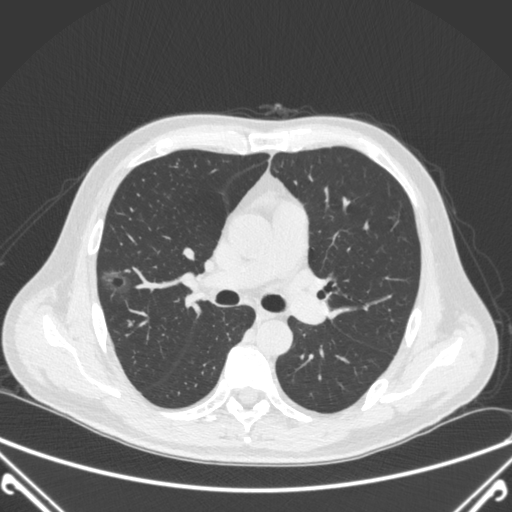
Chest CT, one axial slice. Position 224 of 360 along the scan axis. Lung window (W 1500 / L -600 HU). 1 mm slice thickness. 512 × 512 image matrix. Male patient, age 64 years. From the clinical record (not read from this slice): clinical TNM (as recorded): T1c N0 M0.
Outlined on this slice (bounding box drawn by a radiologist):
- lung tumour (recorded histology: adenocarcinoma): box from (x=100, y=262) to (x=148, y=310) px